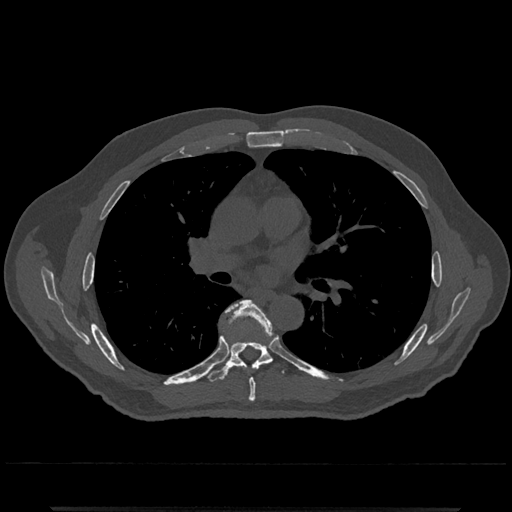
CT including the spine, one axial slice; slice 745 of 797 in the series (ordered by position); reconstruction kernel Br40s/3; bone window (W 1800 / L 400 HU); 0.5 mm slice thickness; 512 × 512 image matrix, field of view 393 × 393 mm. Patient: male, 67 years. Case-level facts recorded for this patient, not image findings: primary cancer: prostate.
Structures marked on this image (semi-automatically segmented with operator editing):
- T6 vertebra: bounding box (x1, y1, x2, y2) in pixels: (226, 300, 271, 402)
- T7 vertebra: (206, 308, 286, 384)